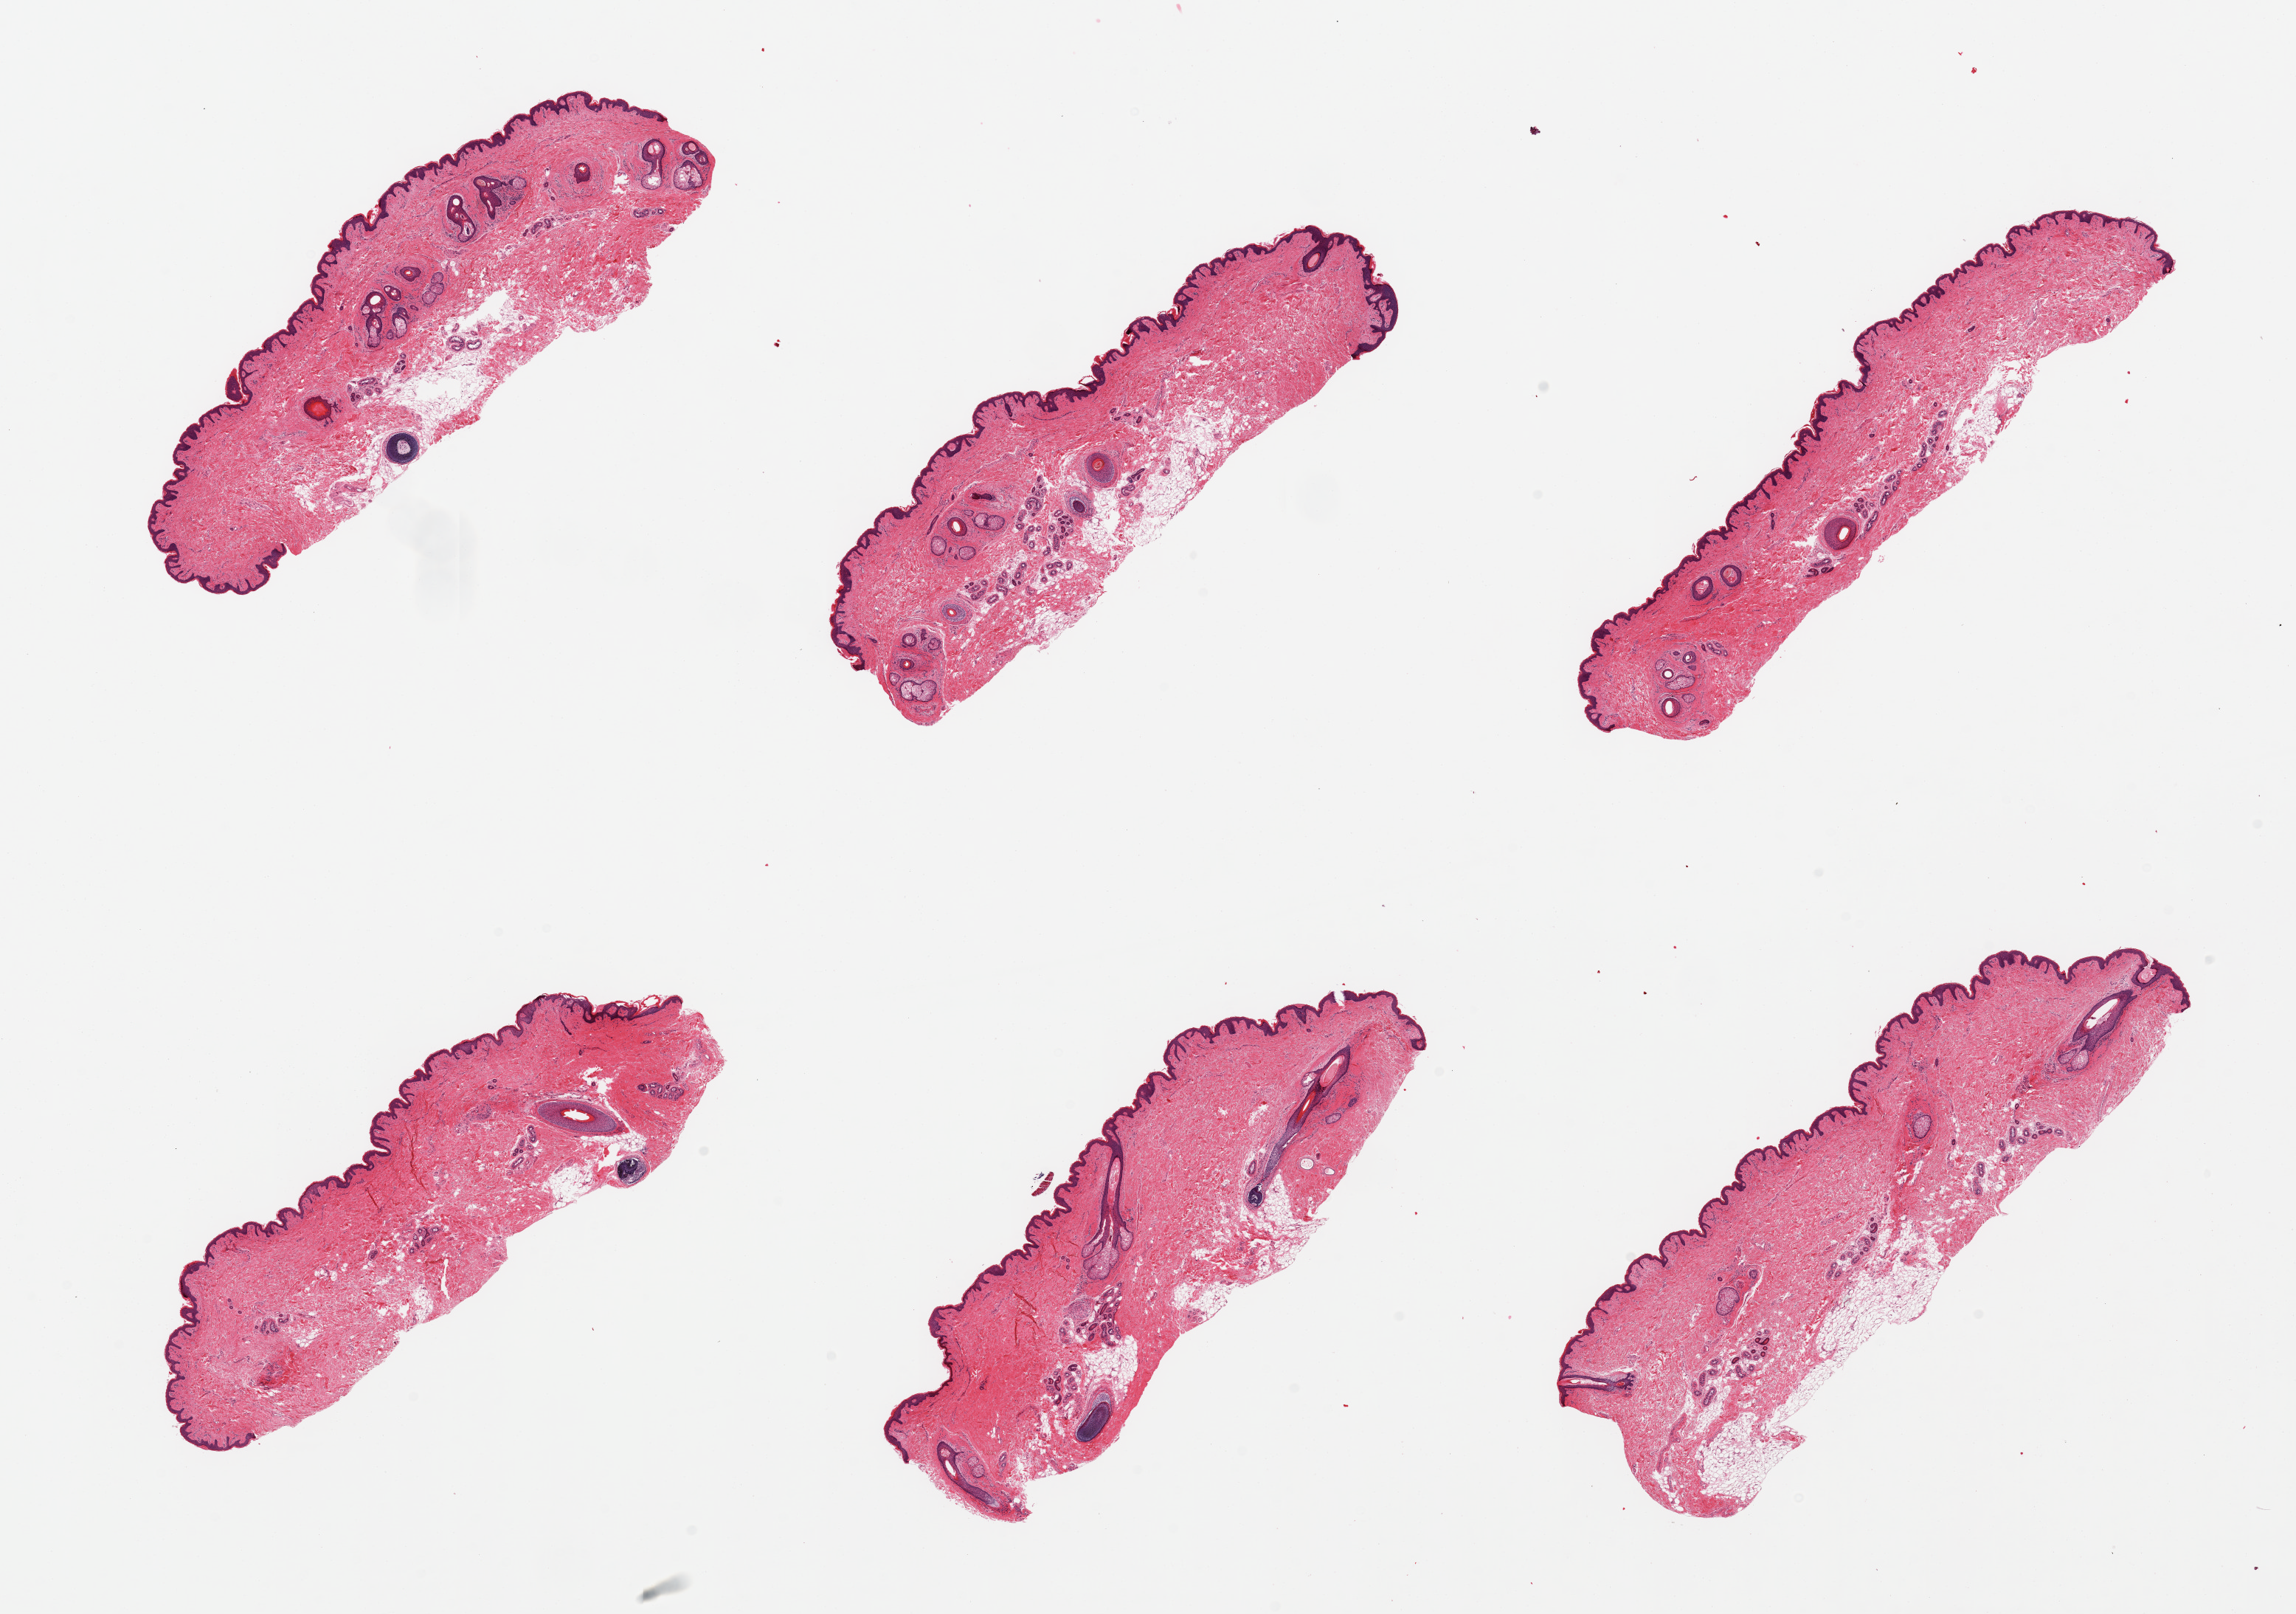
Whole-slide image, H&E stain, whole scanned area (about 24.6 x 17.3 mm) shown as a low-resolution overview. PAXgene-fixed, paraffin-embedded tissue. Target tissue: skin of suprapubic region. Donor tissue sample. Donor sex: male.
Reviewer comment on this tissue sample: 6 pieces; hair bearing skin with 5 to 10% external/internal fat.